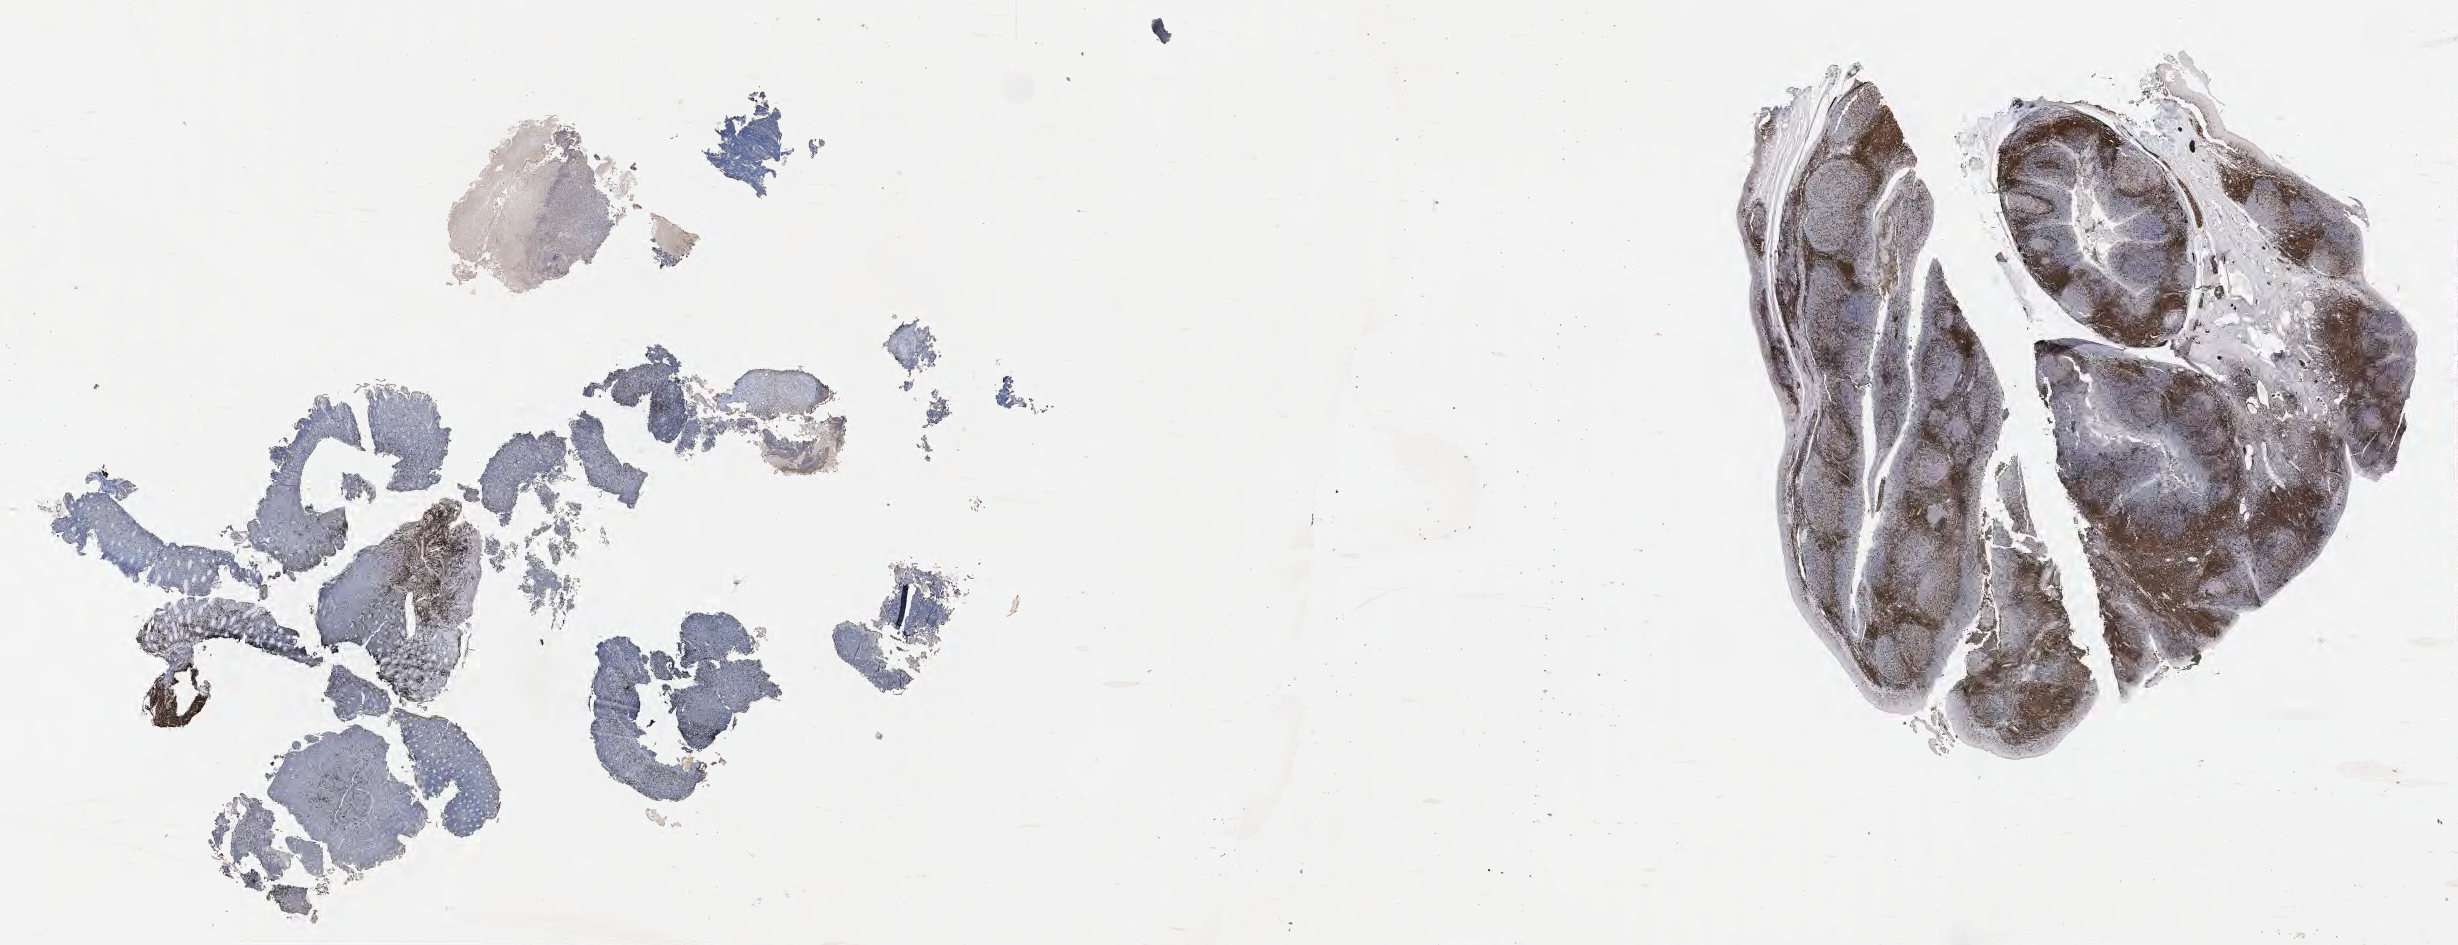
Whole-slide image, immunohistochemical stain for CD3 — a low-resolution overview of the entire scanned area, about 39.7 x 15.3 mm, tumor tissue. Patient male; age 56 years.
Histologic diagnosis: Burkitt lymphoma, NOS.